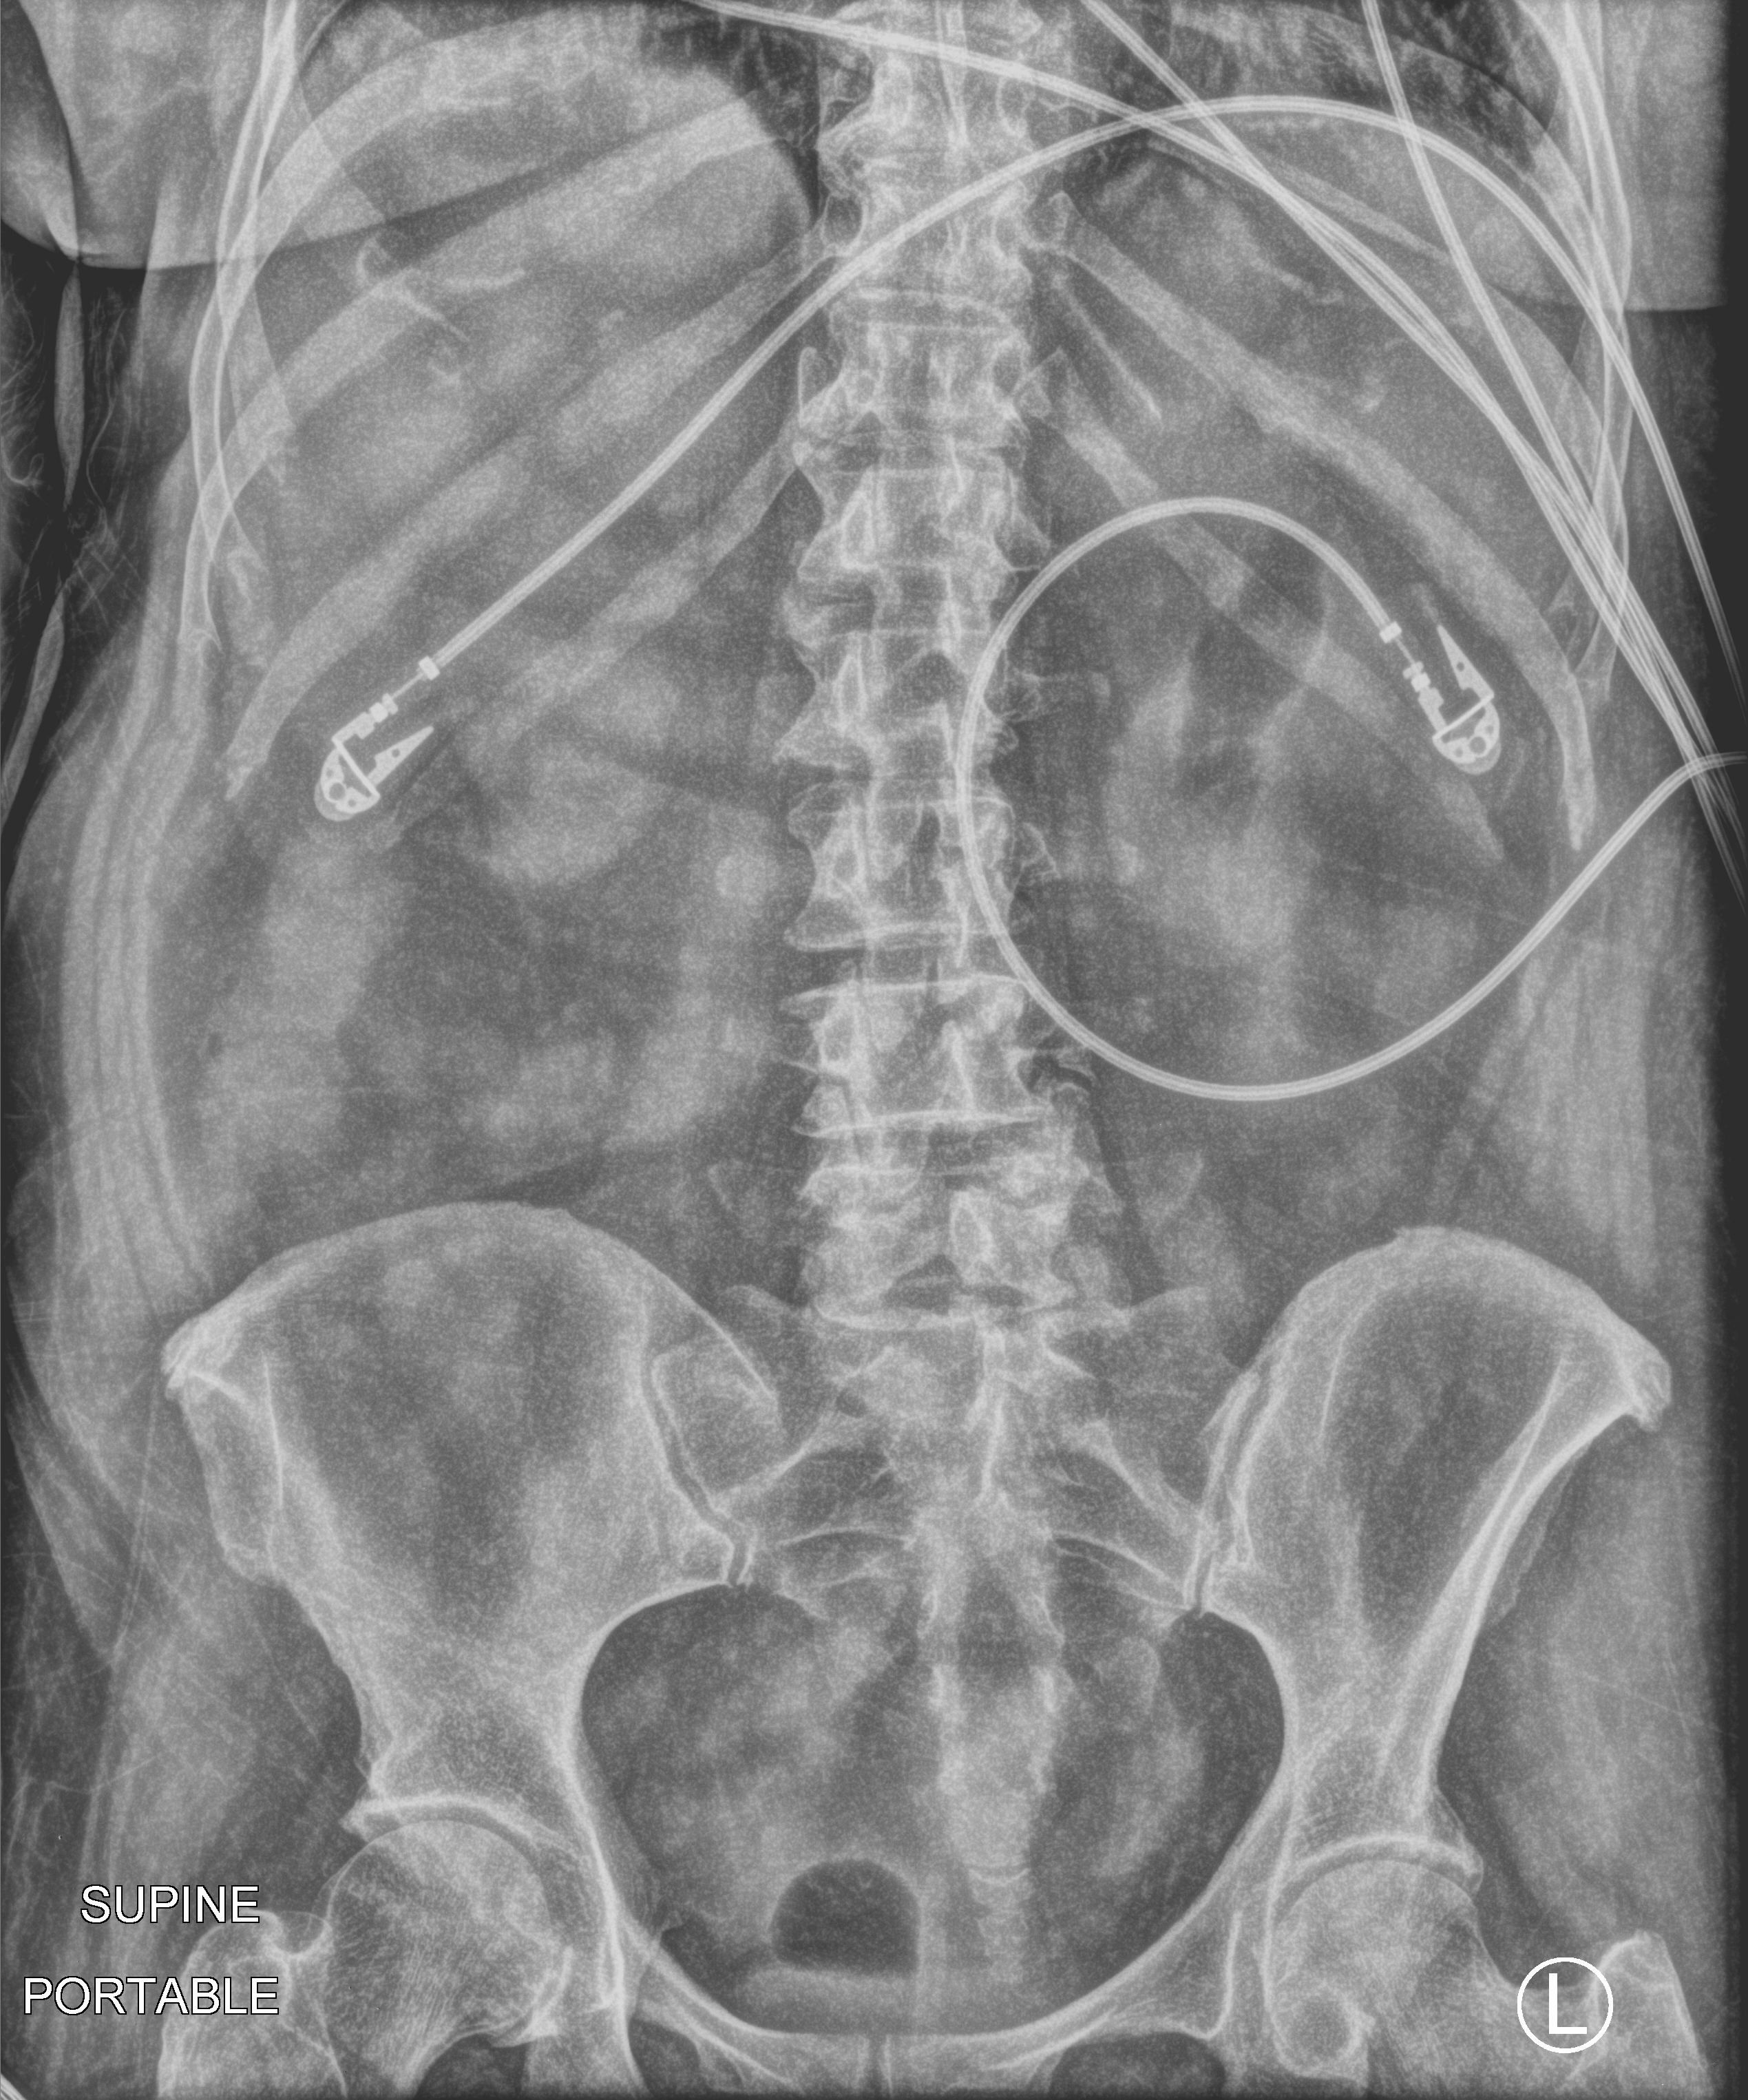
Abdomen X-ray (portable). Patient hospitalised with COVID-19; female, aged 60–74 years.
Admission-level facts for this patient (not findings on this image; timing relative to this image not recorded): smoking status (admission record): former; mechanically ventilated during this hospital stay: yes.